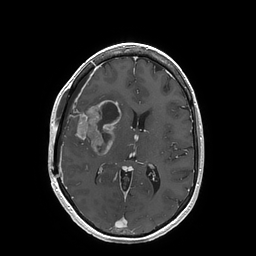
Brain MRI from a brain-tumour surgery series, one axial slice; slice 80 of 202 in the series (ordered by position); T1-weighted post-contrast; 1 mm slice thickness; 256 × 256 image matrix. From the clinical record (not read from this slice): histopathology: Glioblastoma; WHO grade: 4; IDH mutation: no; tumour location: Right Insular.
Structures marked on this image (outlined manually by an expert reader):
- tumour: bounding box [x1, y1, x2, y2] px = [69, 100, 121, 155]